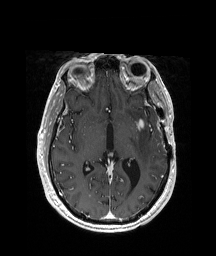
Brain MRI from a brain-tumour surgery series, one axial slice. Slice 110 of 208 in the series (ordered by position). T1-weighted post-contrast. 1 mm slice thickness. 216 × 256 image matrix, field of view 228 × 270 mm. Case-level facts recorded for this patient, not image findings: histopathology: Glioblastoma; WHO grade: 4; IDH mutation: no; tumour location: Left Anterior/Superior Temporal.
Outlined on this slice (expert manual segmentation):
- tumour: bounding box <137,120,144,130> (left, top, right, bottom; pixels)